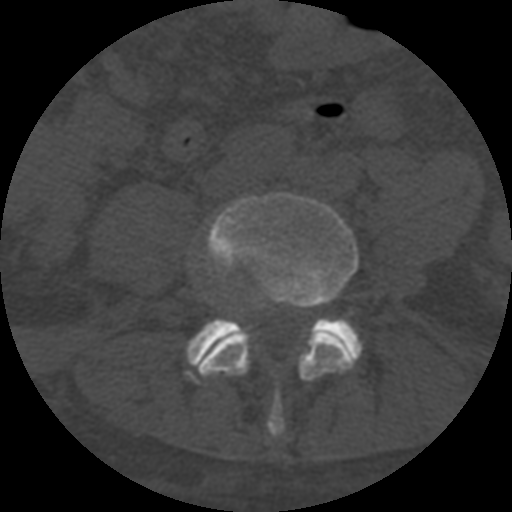
CT including the spine, one axial slice; position 199 of 708 along the scan axis; reconstruction kernel STANDARD; 120 kVp; one of 3 acquisitions stored at this slice position; bone window (W 1800 / L 400 HU); 1.25 mm slice thickness; 512 × 512 image matrix. Patient age 55 years. From the clinical record (not read from this slice): primary cancer: colon; vertebrae with lytic lesions (as recorded): T12, L1, L5.
Annotated regions visible in this slice (semi-automatically segmented with operator editing):
- L4 vertebra: bounding box <198,192,359,437> (left, top, right, bottom; pixels)
- L5 vertebra: <186,319,362,370>